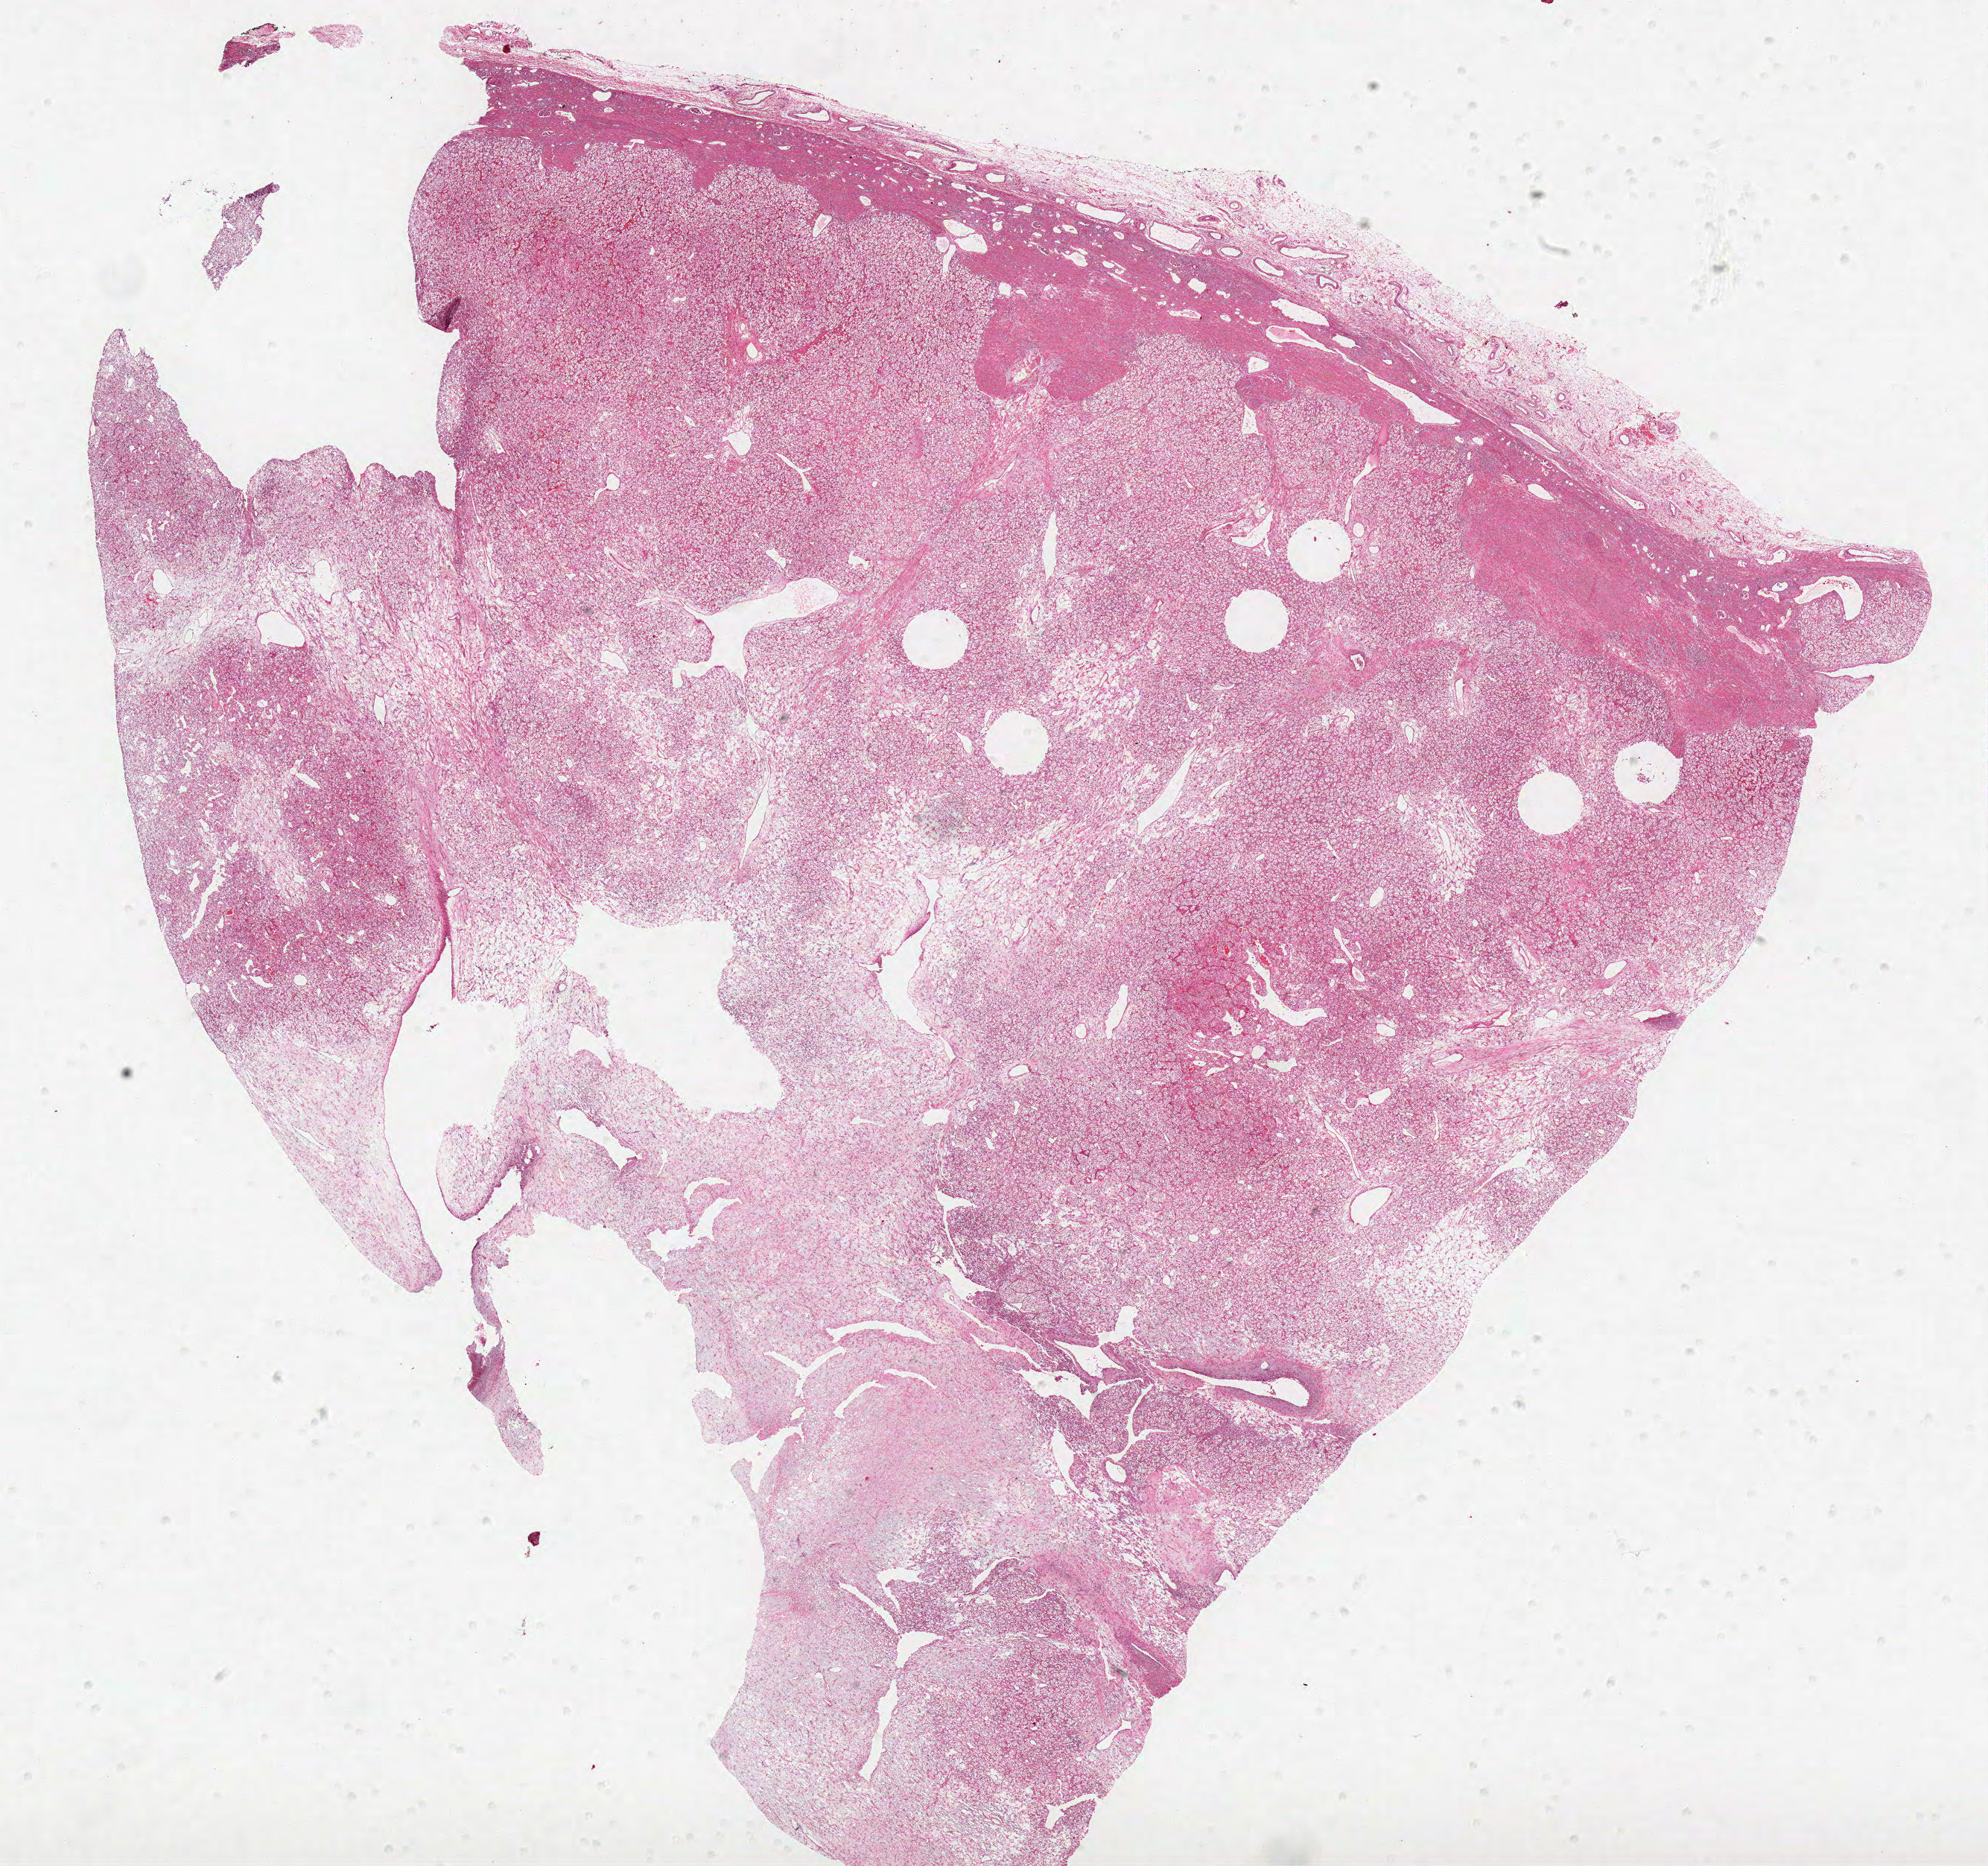
Digitized H&E tissue section (whole slide), a low-resolution overview of the entire scanned area, about 21.3 x 20.0 mm, formalin-fixed paraffin-embedded (FFPE) diagnostic section, sample: primary tumour, kidney. Female patient; age at initial diagnosis 46 years. Histologic grade: G3 (poorly differentiated).
- TNM: T1a NX M0
- AJCC pathologic stage: I
- histologic diagnosis: Clear cell adenocarcinoma, NOS